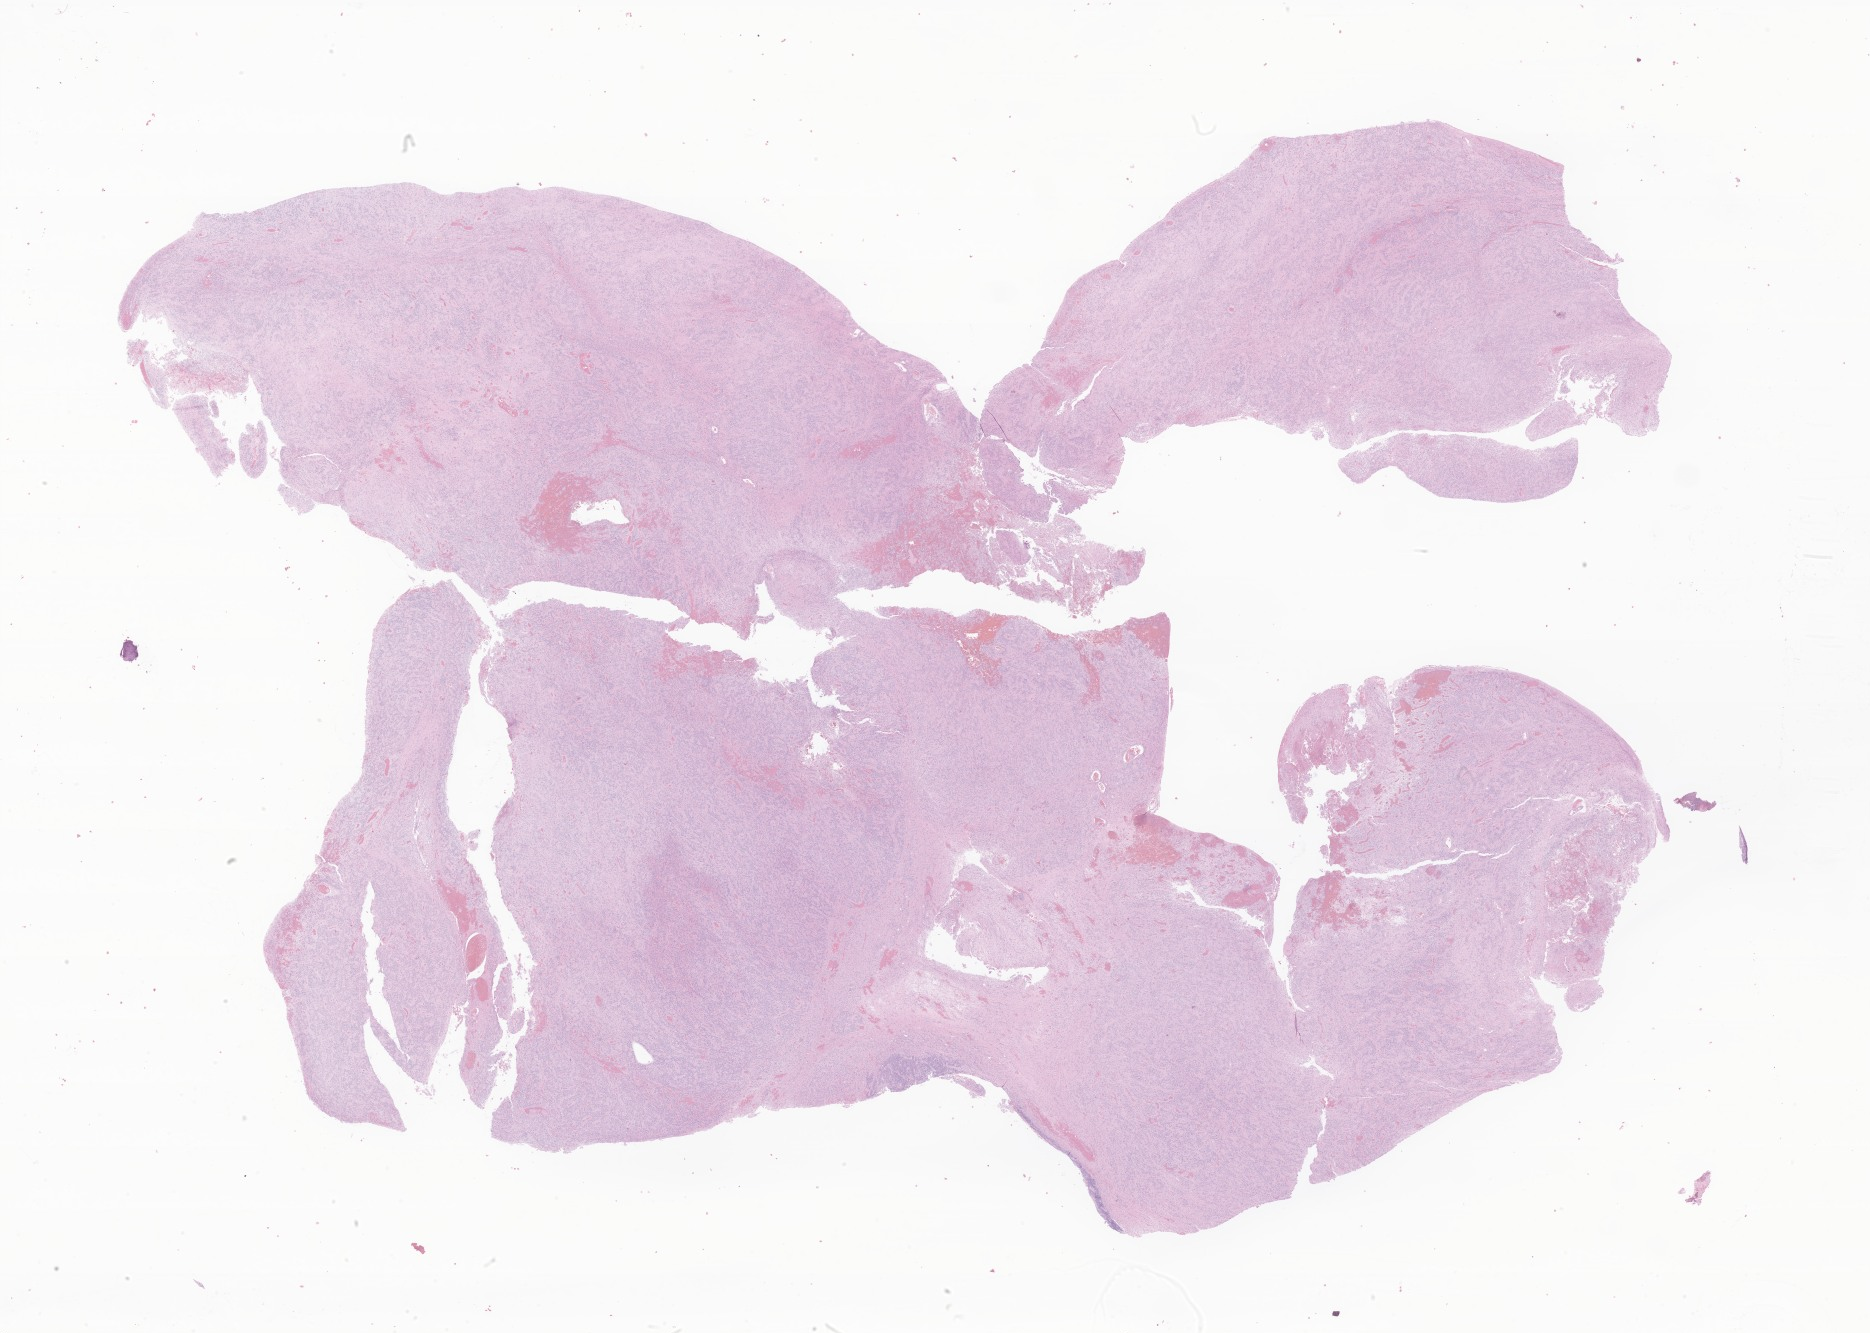
Hematoxylin and eosin (H&E) whole-slide image of tumor tissue from the brain stem — low-resolution overview of the scanned area, about 31.5 x 22.5 mm; FFPE section. Patient female; age 35 months.
Diagnosis: Ependymoma, NOS.